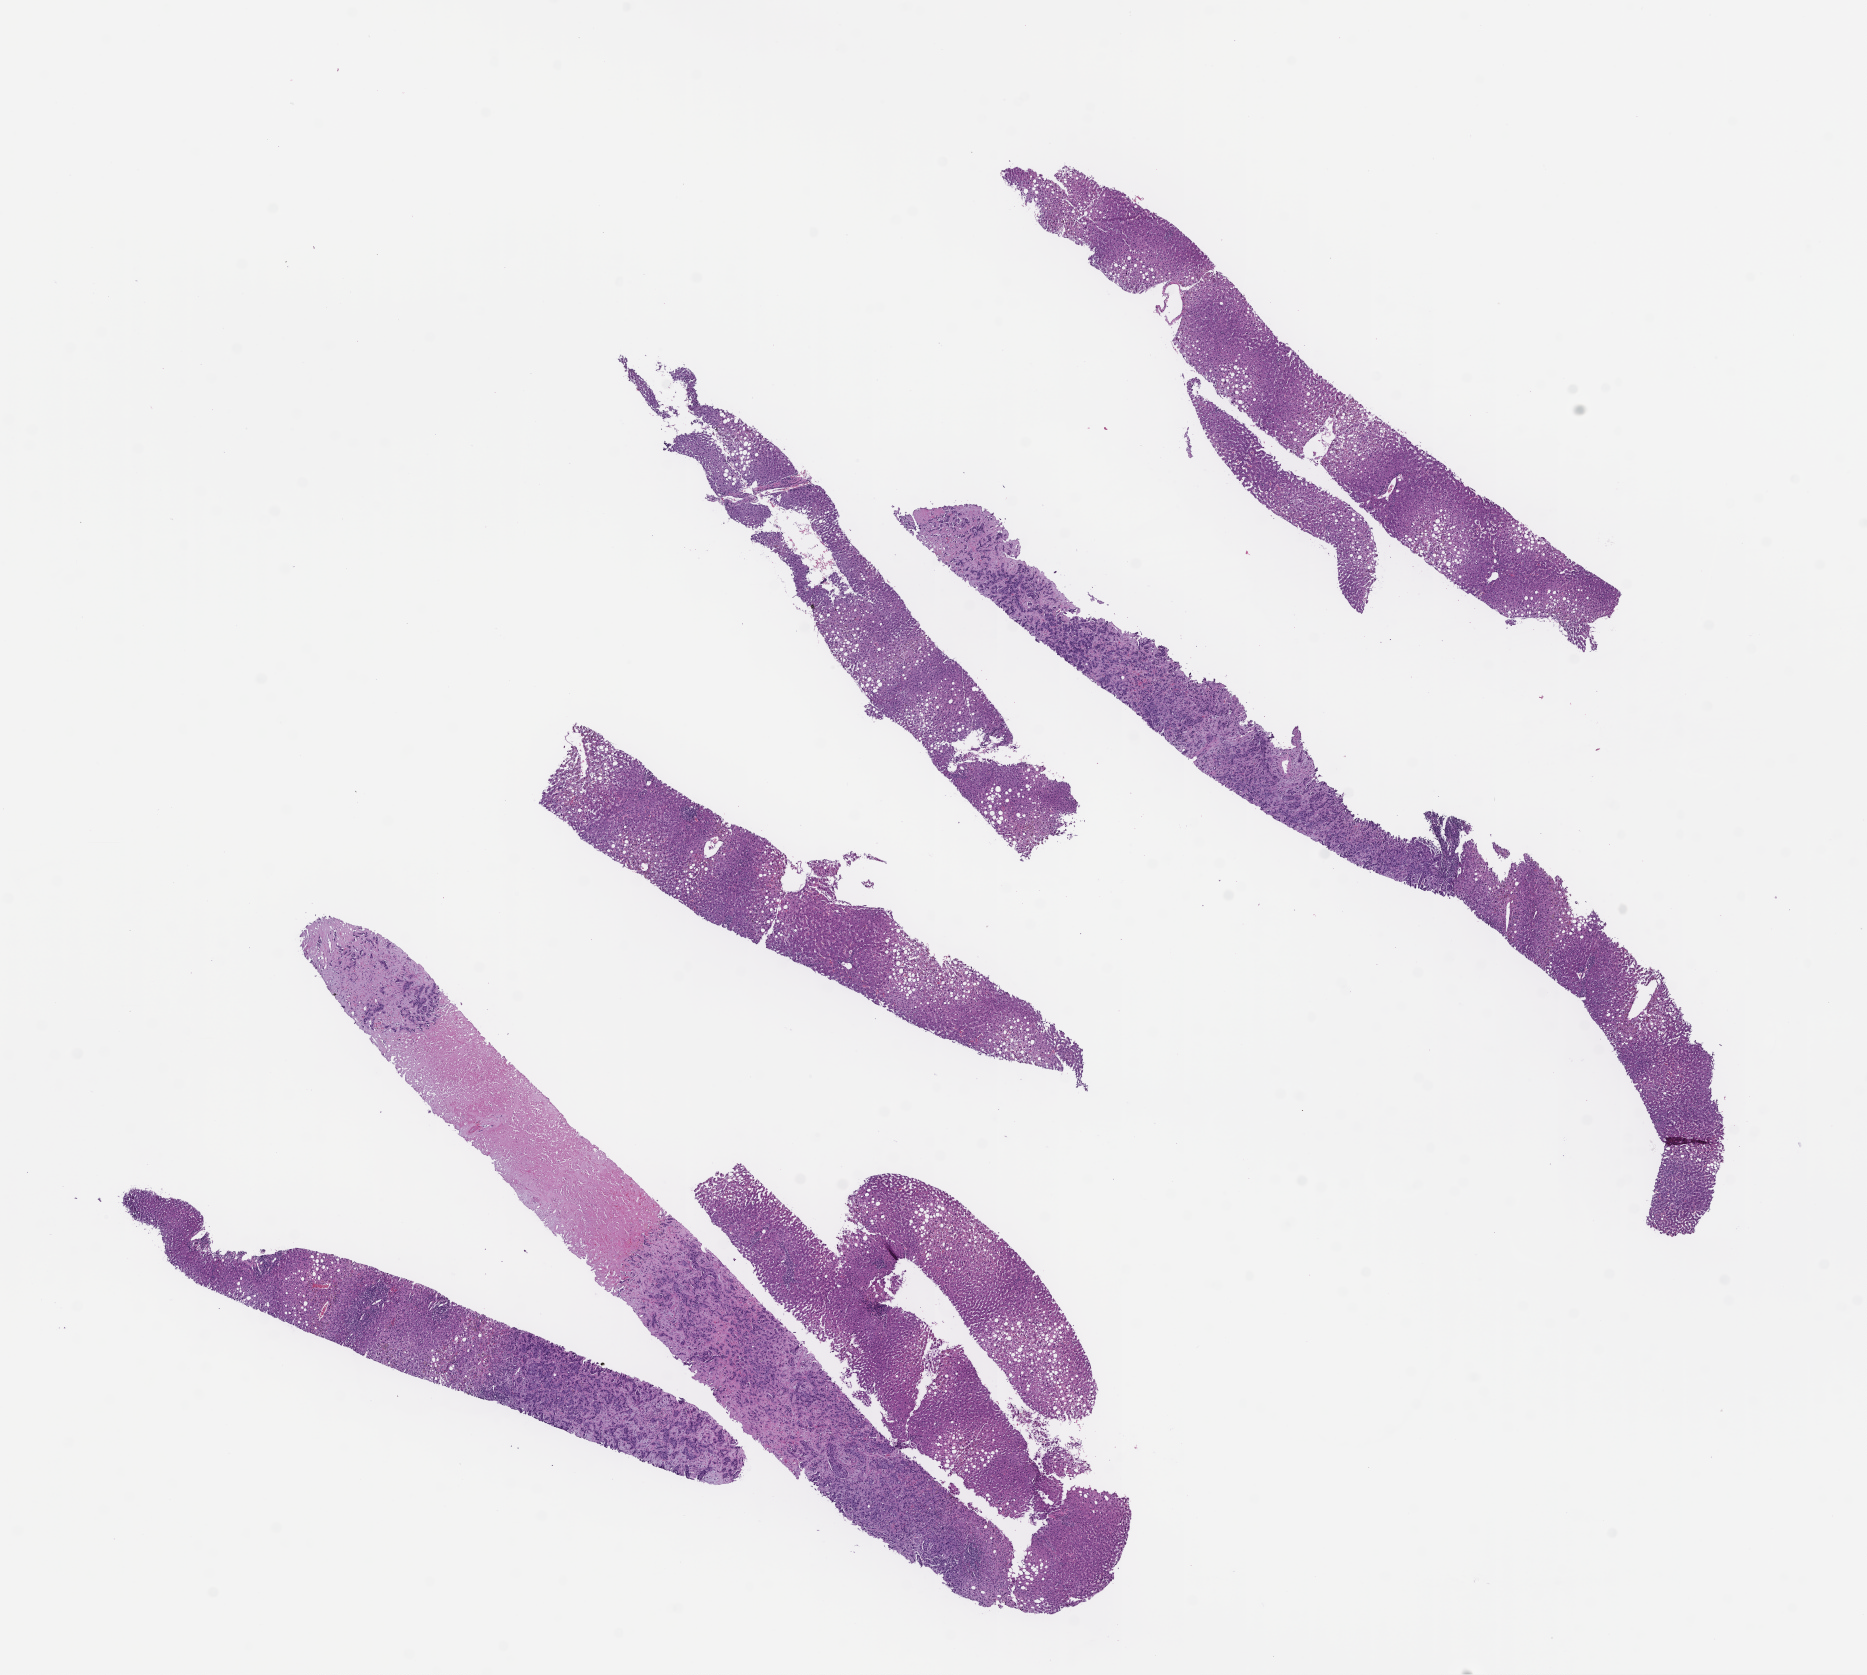
H&E whole-slide image, a low-resolution overview of the entire scanned area, about 15.1 x 13.5 mm. FFPE section. Specimen time point: archival tissue. Patient sex: female.
This section: metastasis (sampled organ not recorded). Patient diagnosis (primary): Invasive Breast Carcinoma.